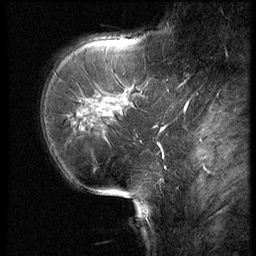
Breast MRI (dynamic contrast-enhanced), one sagittal slice; slice 19 of 62 in the series (ordered by position); 3 images stored at this slice position (order not interpretable as contrast timing); 1.5 T; TE 4.2 ms, TR 9 ms; 2.5 mm slice thickness; 256 × 256 image matrix, field of view 180 × 180 mm. Female patient, age 62 years. From the clinical record (not read from this slice): setting: breast cancer imaged before/during neoadjuvant chemotherapy; receptor status: HR-positive, HER2-negative.
Outlined on this slice (semi-automatically segmented with operator editing):
- analysis volume of interest (the breast-tissue region the enhancement analysis was run in; not a lesion): box from (x=56, y=62) to (x=154, y=155) px
- tumour enhancement mask (voxels above the 140 % enhancement threshold inside the analysis volume of interest): (x=81, y=110)–(x=110, y=130)